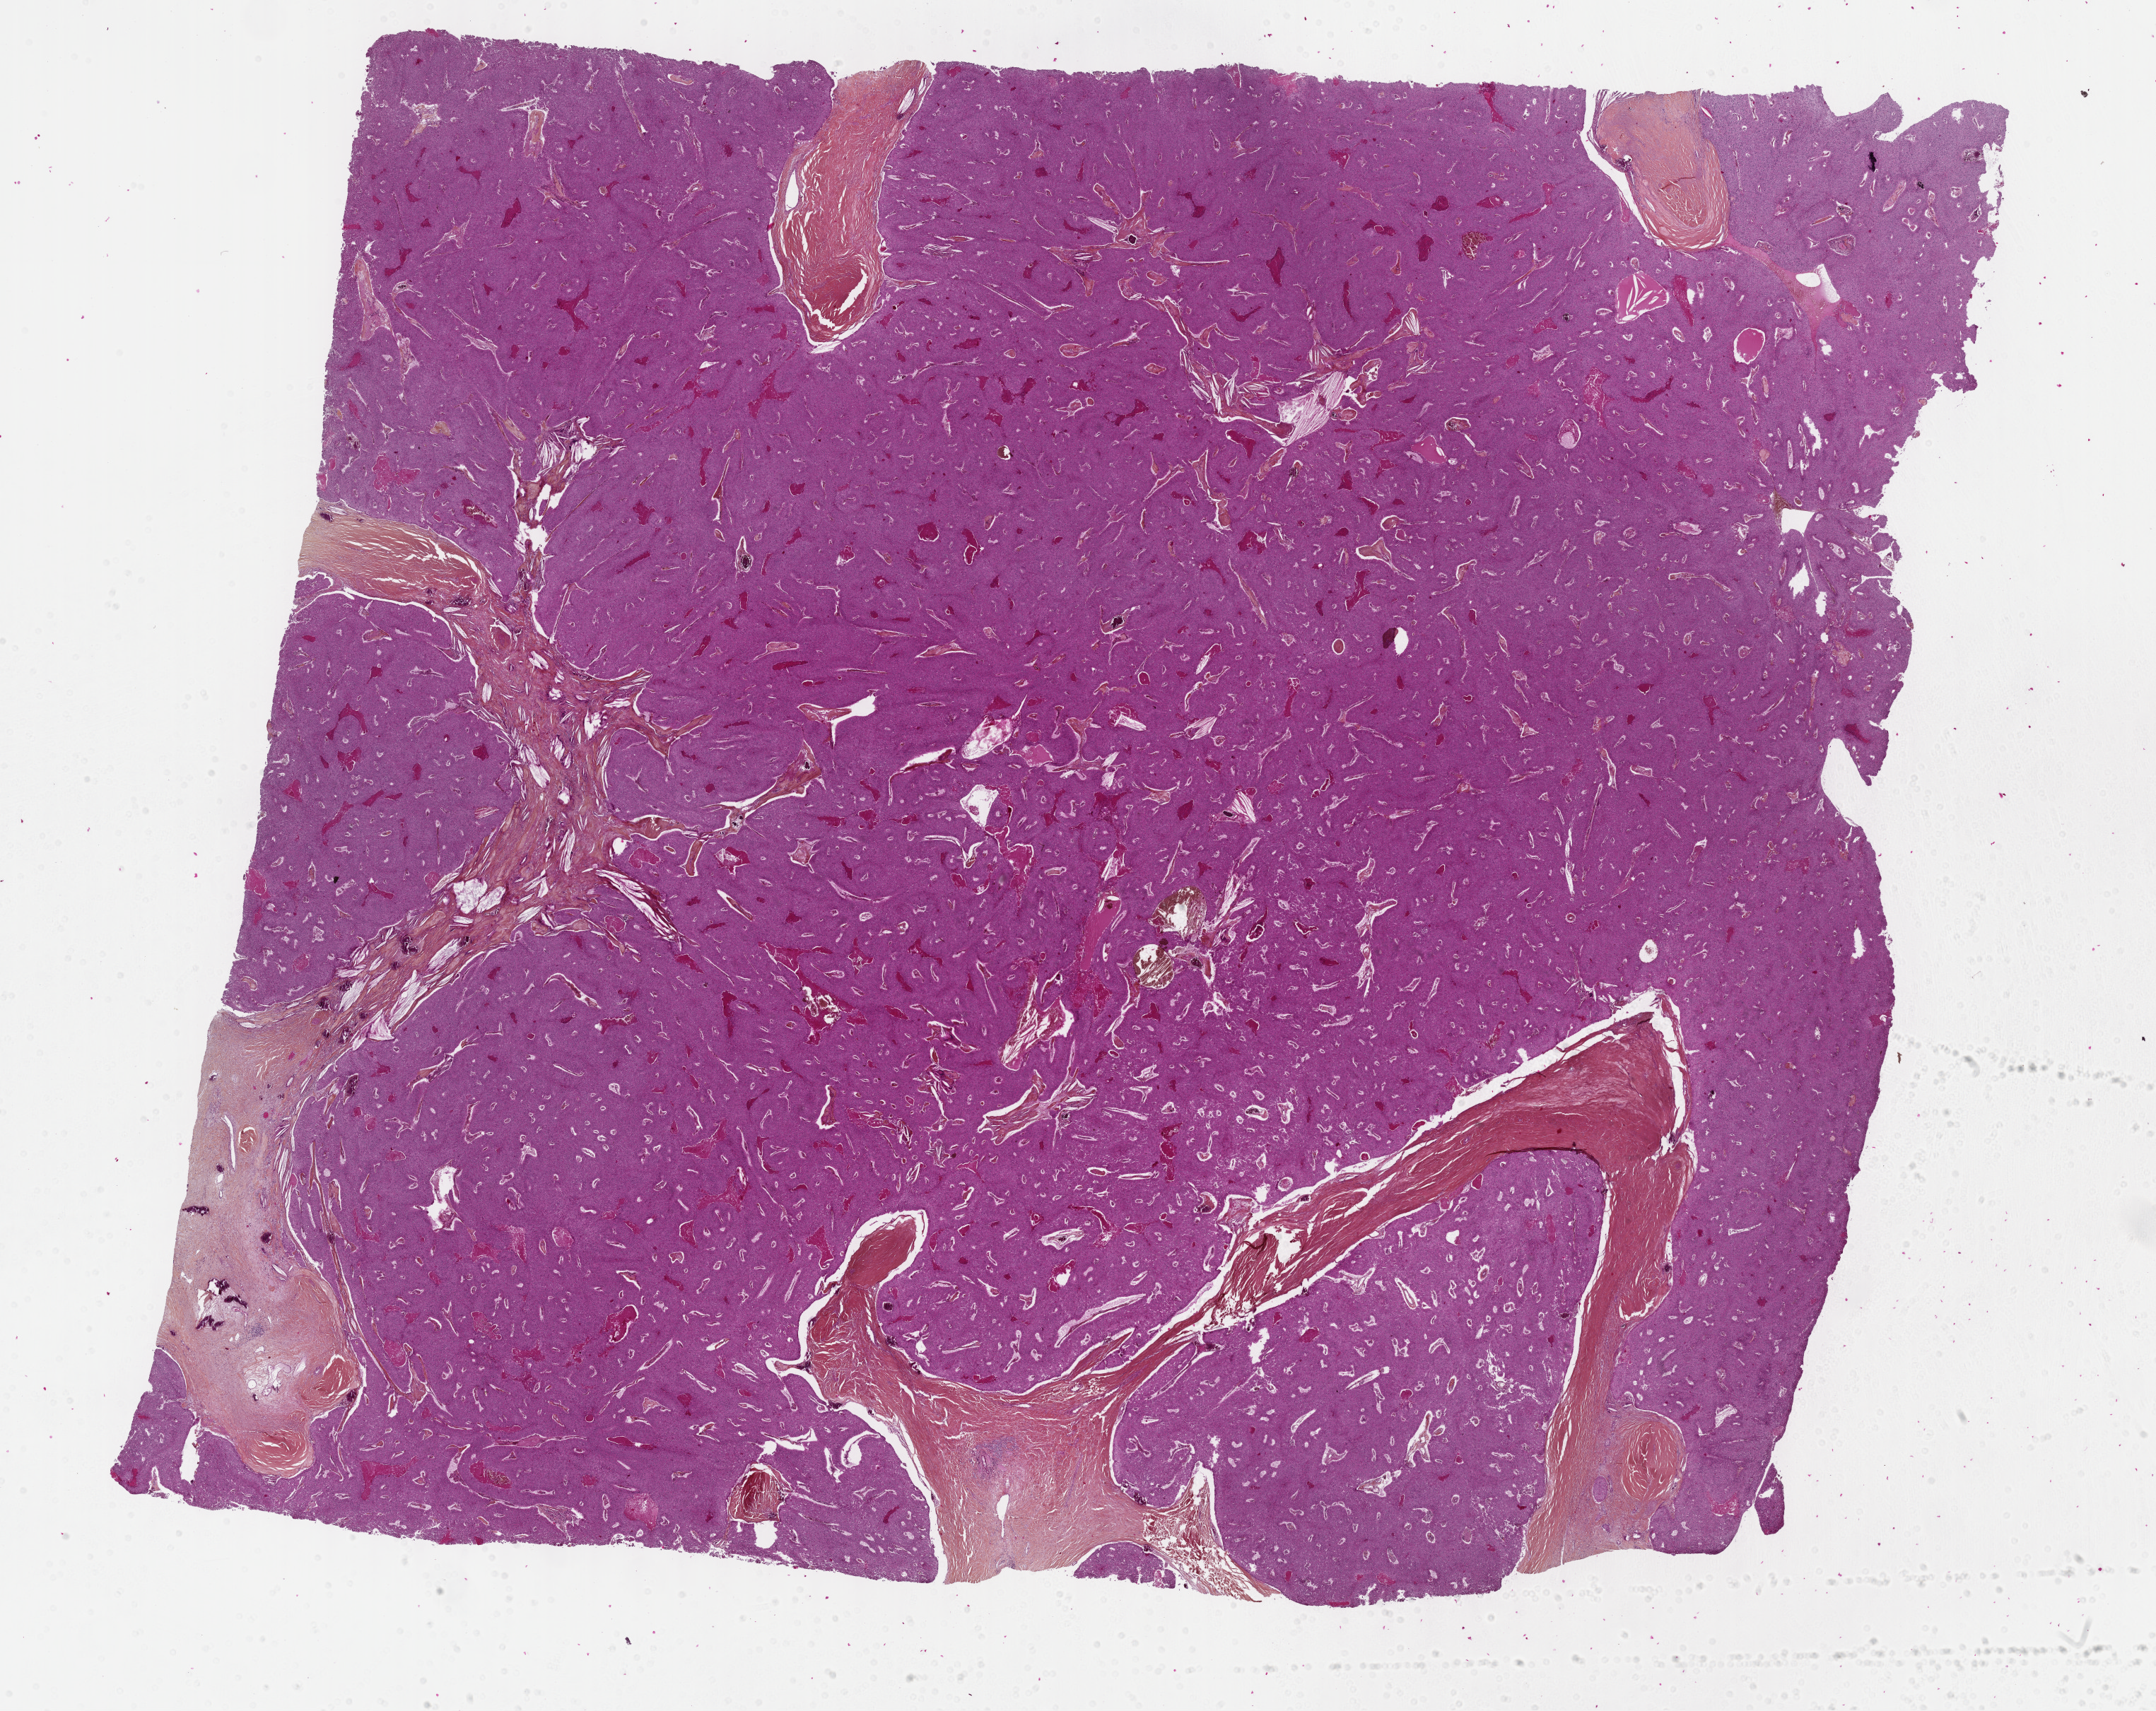
Whole-slide histology image, H&E, low-resolution overview of the scanned area, about 24.7 x 19.6 mm (from a 40x scan). Formalin-fixed paraffin-embedded (FFPE) diagnostic section. Sample: primary tumour, thymus. Female patient; age at initial diagnosis 40 years.
• histologic diagnosis: Thymoma, type B3, malignant